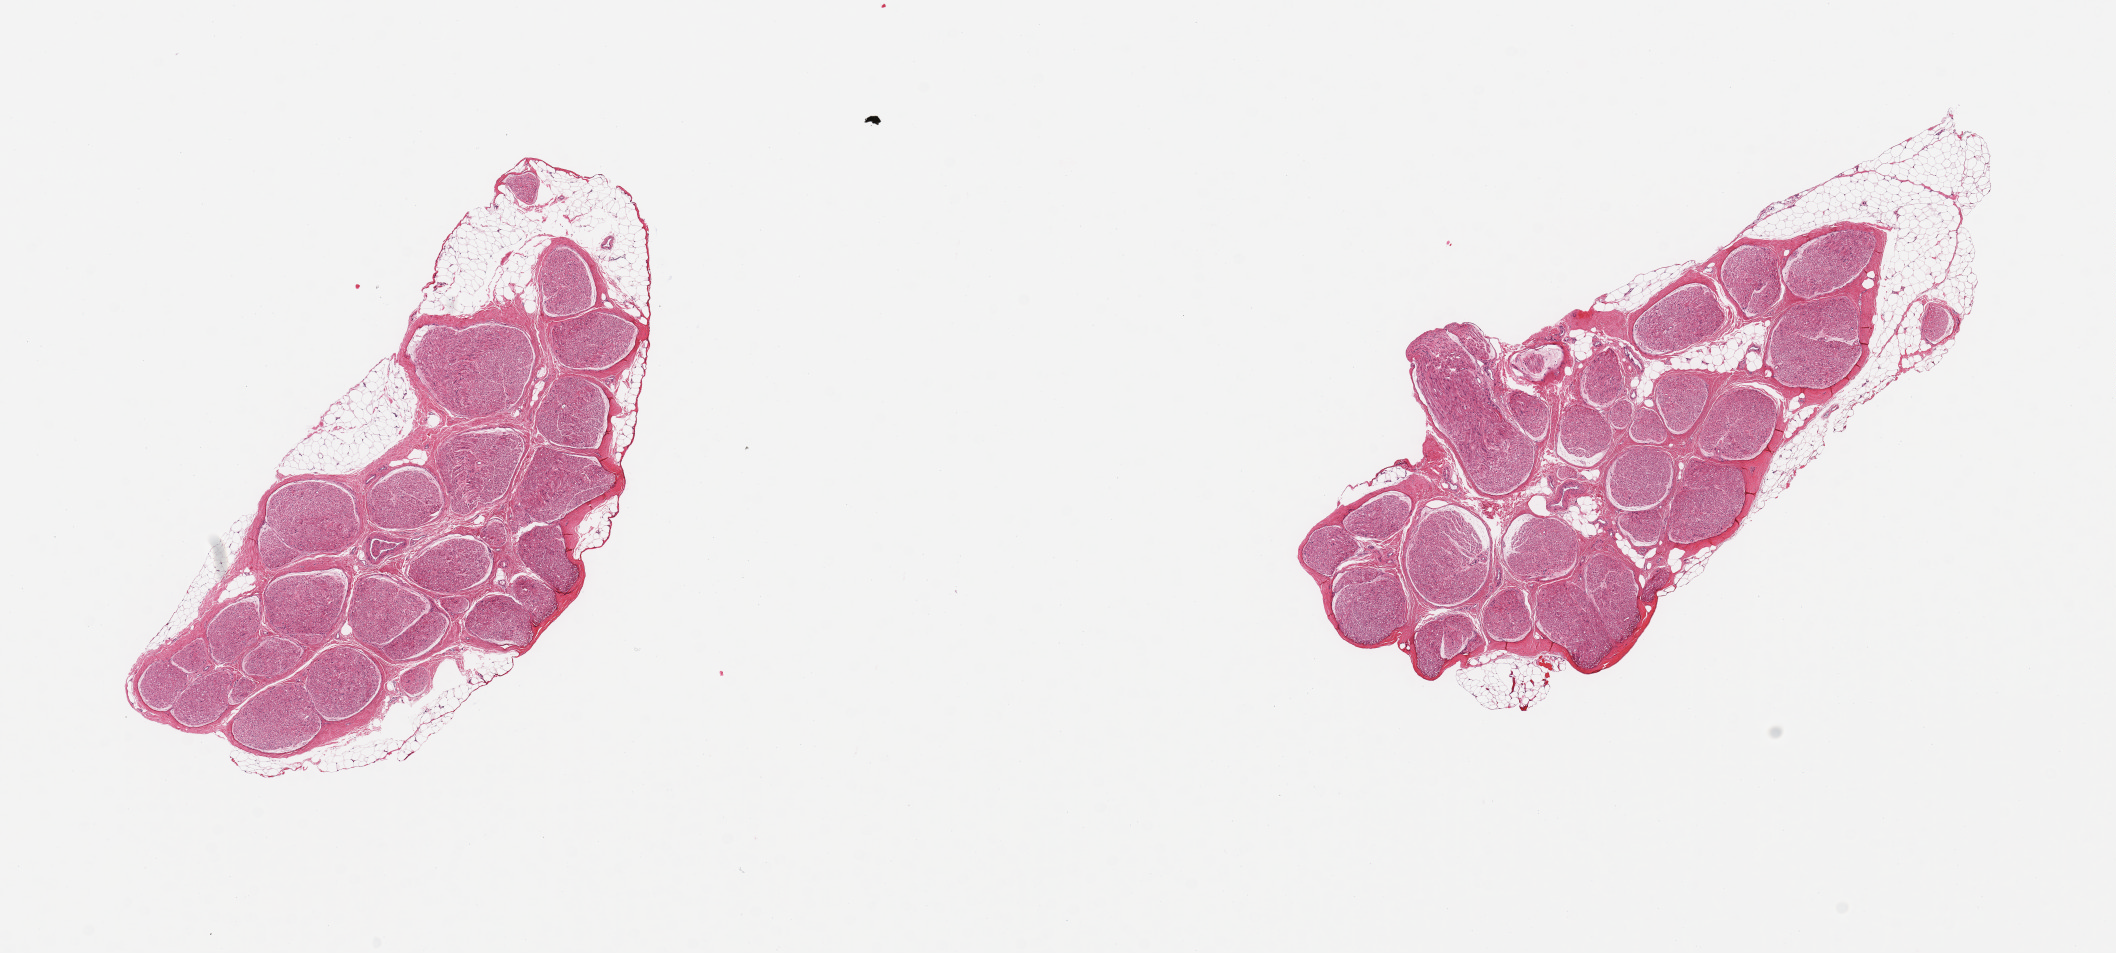
Digitized haematoxylin and eosin-stained section — shown as a low-resolution overview of the whole scanned area (about 16.7 x 7.5 mm); PAXgene-fixed, paraffin-embedded tissue; section of tibial nerve (target tissue); tissue donor sample. Donor: female.
* review note (as recorded): 2 pieces, nubbins of adherent fat up to ~1mm